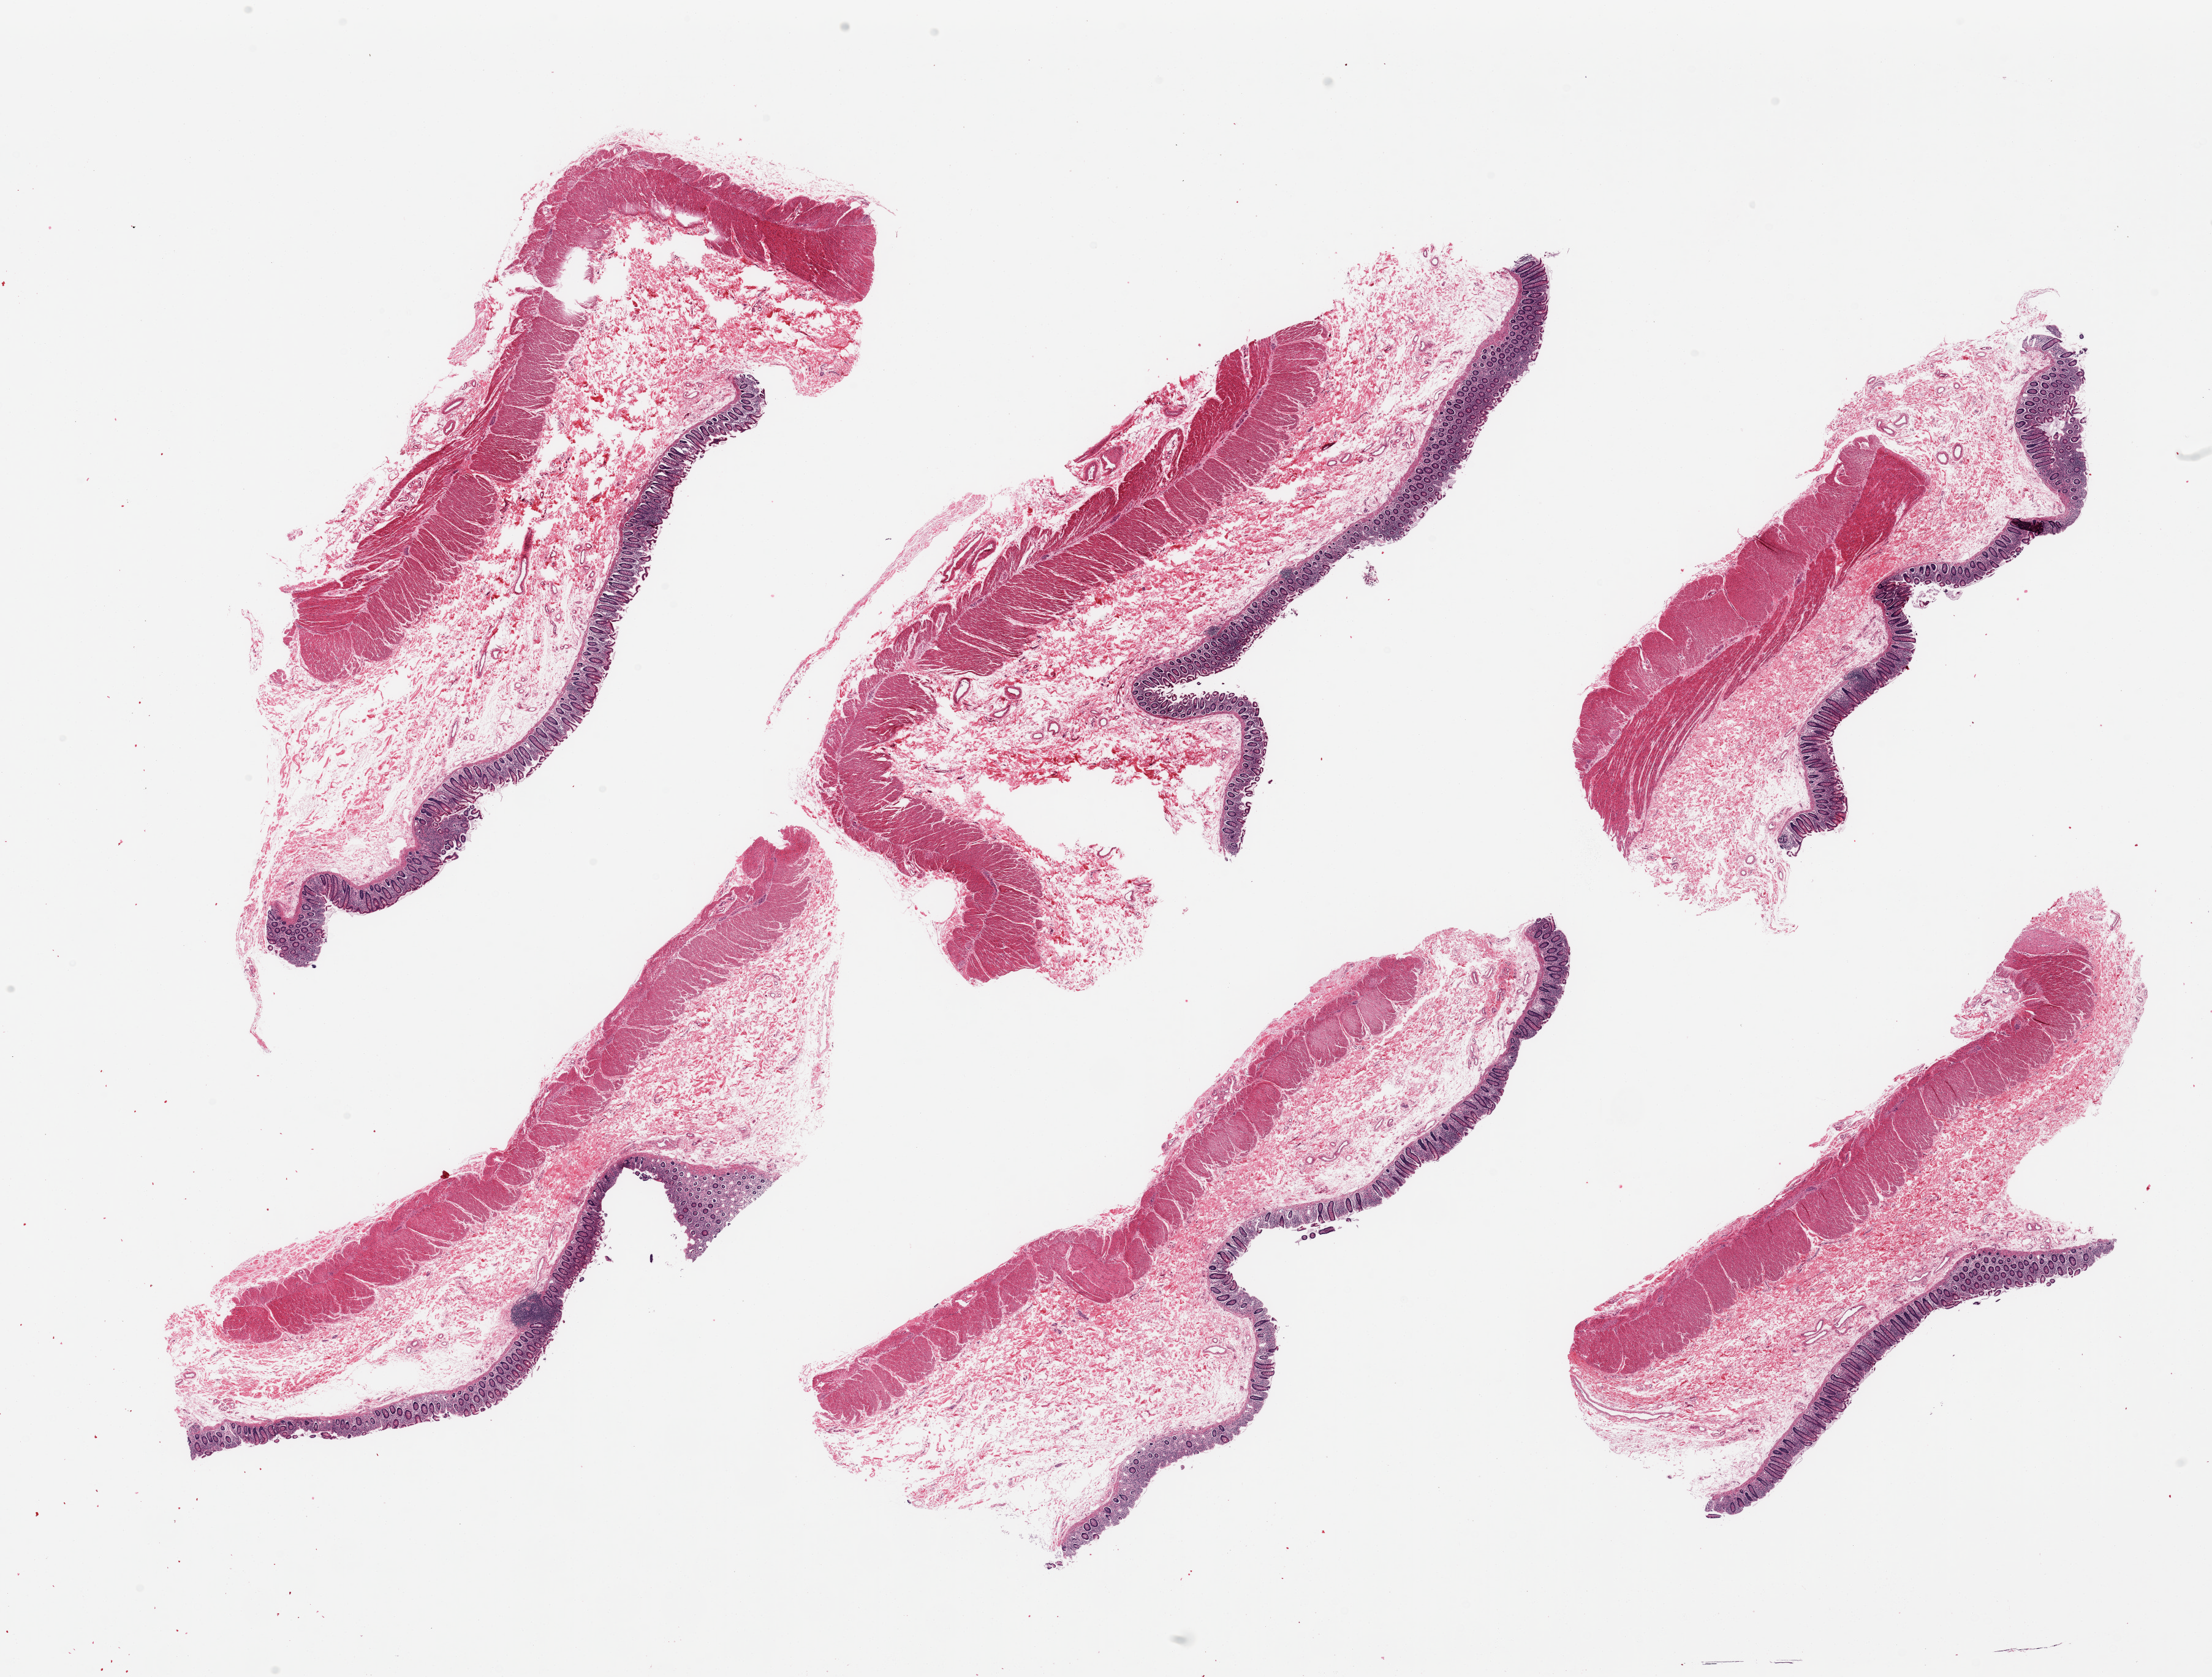
Haematoxylin and eosin whole-slide image — whole scanned area (about 28.5 x 21.6 mm, slide scanned at 20x) shown as a low-resolution overview. PAXgene-fixed paraffin-embedded (PFPE) section. Target tissue: transverse colon. Tissue donor sample. Donor: female.
Reviewer comment on this tissue sample: 6 pieces, target mucosa up to ~ 0.5mm, ~10-15% thickness.